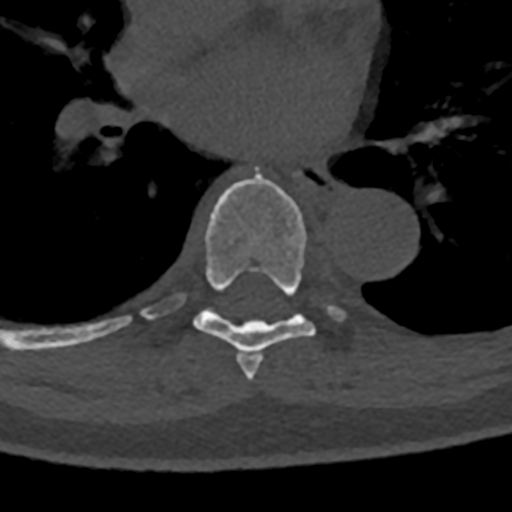
CT including the spine, one axial slice. Position 760 of 797 along the scan axis. Reconstruction kernel Br40s/3. 120 kVp. Bone window (W 1800 / L 400 HU). 0.5 mm slice thickness. 512 × 512 image matrix, field of view 160 × 160 mm. Male patient, age 74 years. From the clinical record (not read from this slice): primary cancer: renal.
Outlined on this slice (semi-automatically segmented with operator editing):
- T6 vertebra: bounding box <245,355,263,380> (left, top, right, bottom; pixels)
- T7 vertebra: <70,172,345,372>
- T8 vertebra: <71,331,107,344>